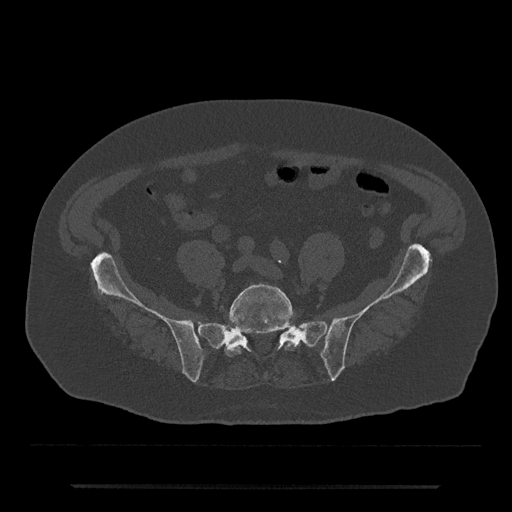
CT including the spine, one axial slice; slice 262 of 797 in the series (ordered by position); reconstruction kernel Br40s/3; 120 kVp; bone window (W 1800 / L 400 HU); 0.5 mm slice thickness; 512 × 512 image matrix, field of view 434 × 434 mm. Patient: male, 80 years. From the clinical record (not read from this slice): primary cancer: prostate; vertebrae with lytic lesions (as recorded): L1, T11.
Annotated regions visible in this slice (semi-automatic segmentation, software-assisted and operator-edited):
- L5 vertebra: bounding box <225,284,295,357> (left, top, right, bottom; pixels)